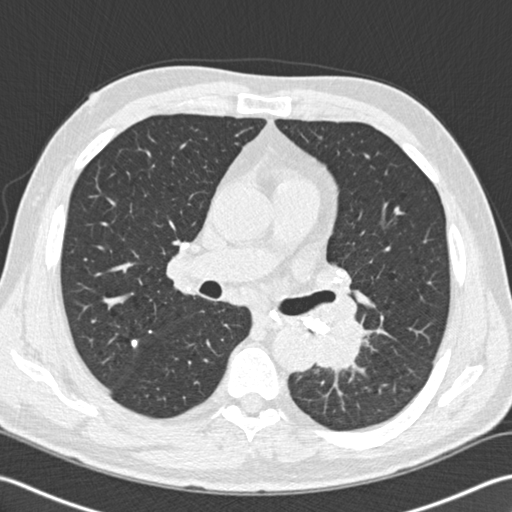
Low-dose screening chest CT, one axial slice. Slice 101 of 170 in the series (ordered by position). Lung window (W 1500 / L -600 HU). 2 mm slice thickness. 512 × 512 image matrix.
Outlined on this slice (expert manual segmentation):
- lesion 1 (tumor, lower lobe of left lung): bounding box [x1, y1, x2, y2] px = [317, 318, 365, 371]